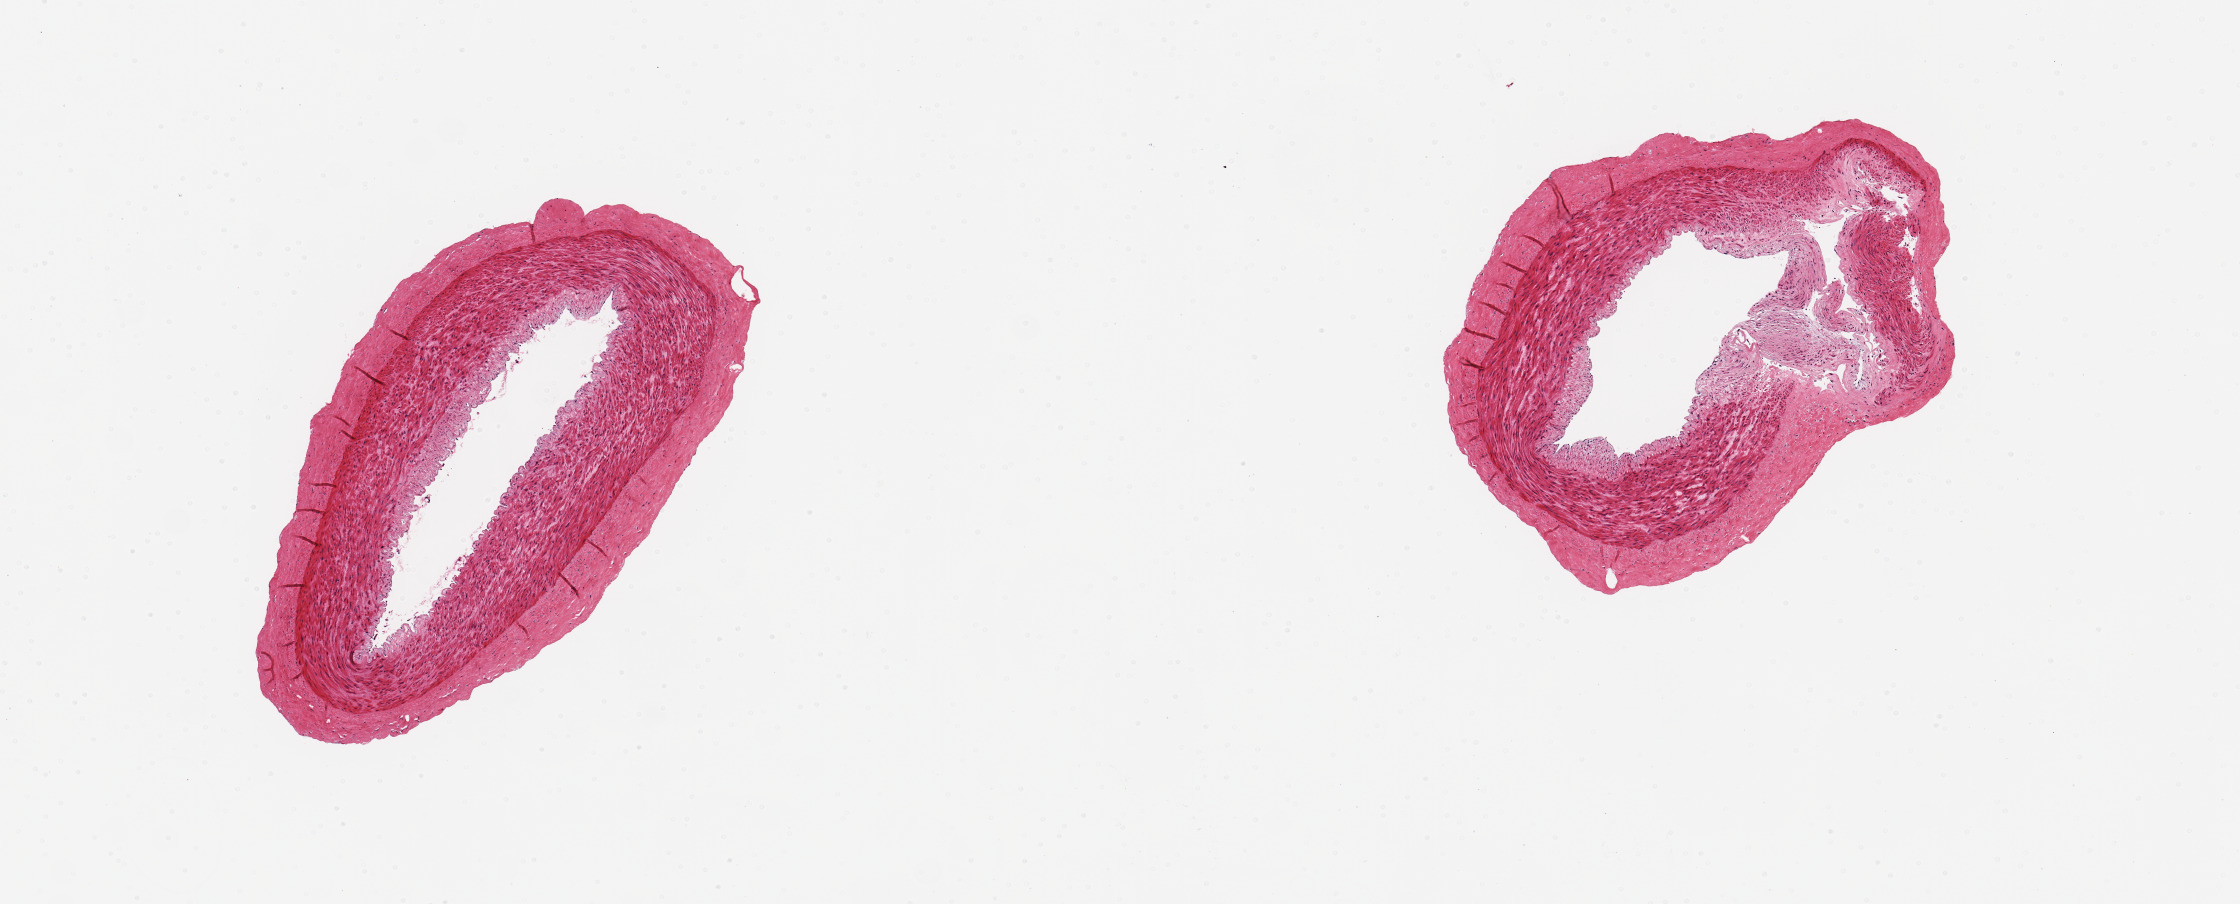
Whole-slide image, H&E stain, shown as a low-resolution overview of the whole scanned area (about 8.9 x 3.6 mm), PAXgene-fixed paraffin-embedded (PFPE) section, section of tibial artery (target tissue), tissue donor sample. Donor sex: male.
Pathologist's review note for this sample: 2 pieces, 1.5 ??? 2 mm diameter; no plaques; no extraneous adipose tissue.